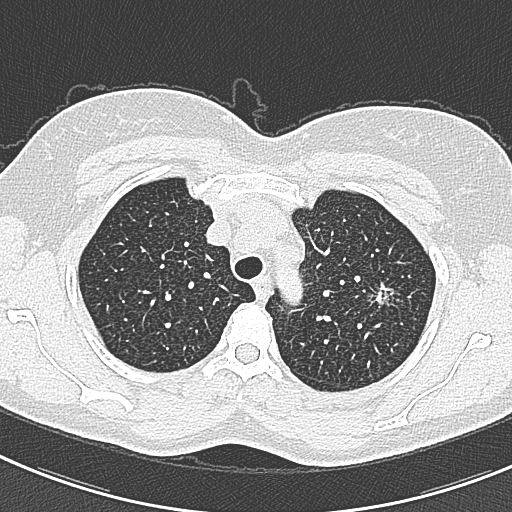
Low-dose screening chest CT, axial slice. First (baseline) screen. Lung window (W 1500 / L -600 HU). 1 mm slice thickness. 512 × 512 image matrix. Female, age 57 years at enrolment.
Expert-annotated lung lesion, box from (x=363, y=275) to (x=412, y=320) px. The screening reader recorded 2 non-calcified nodules or masses ≥4 mm on this exam (right lower lobe, left upper lobe); which of them this box marks is not recorded. Later outcome: lung cancer diagnosed 198 days after this screen — adenocarcinoma, NOS, left upper lobe, well differentiated (G1), stage IA (AJCC 6th edition), 10 mm at pathology.